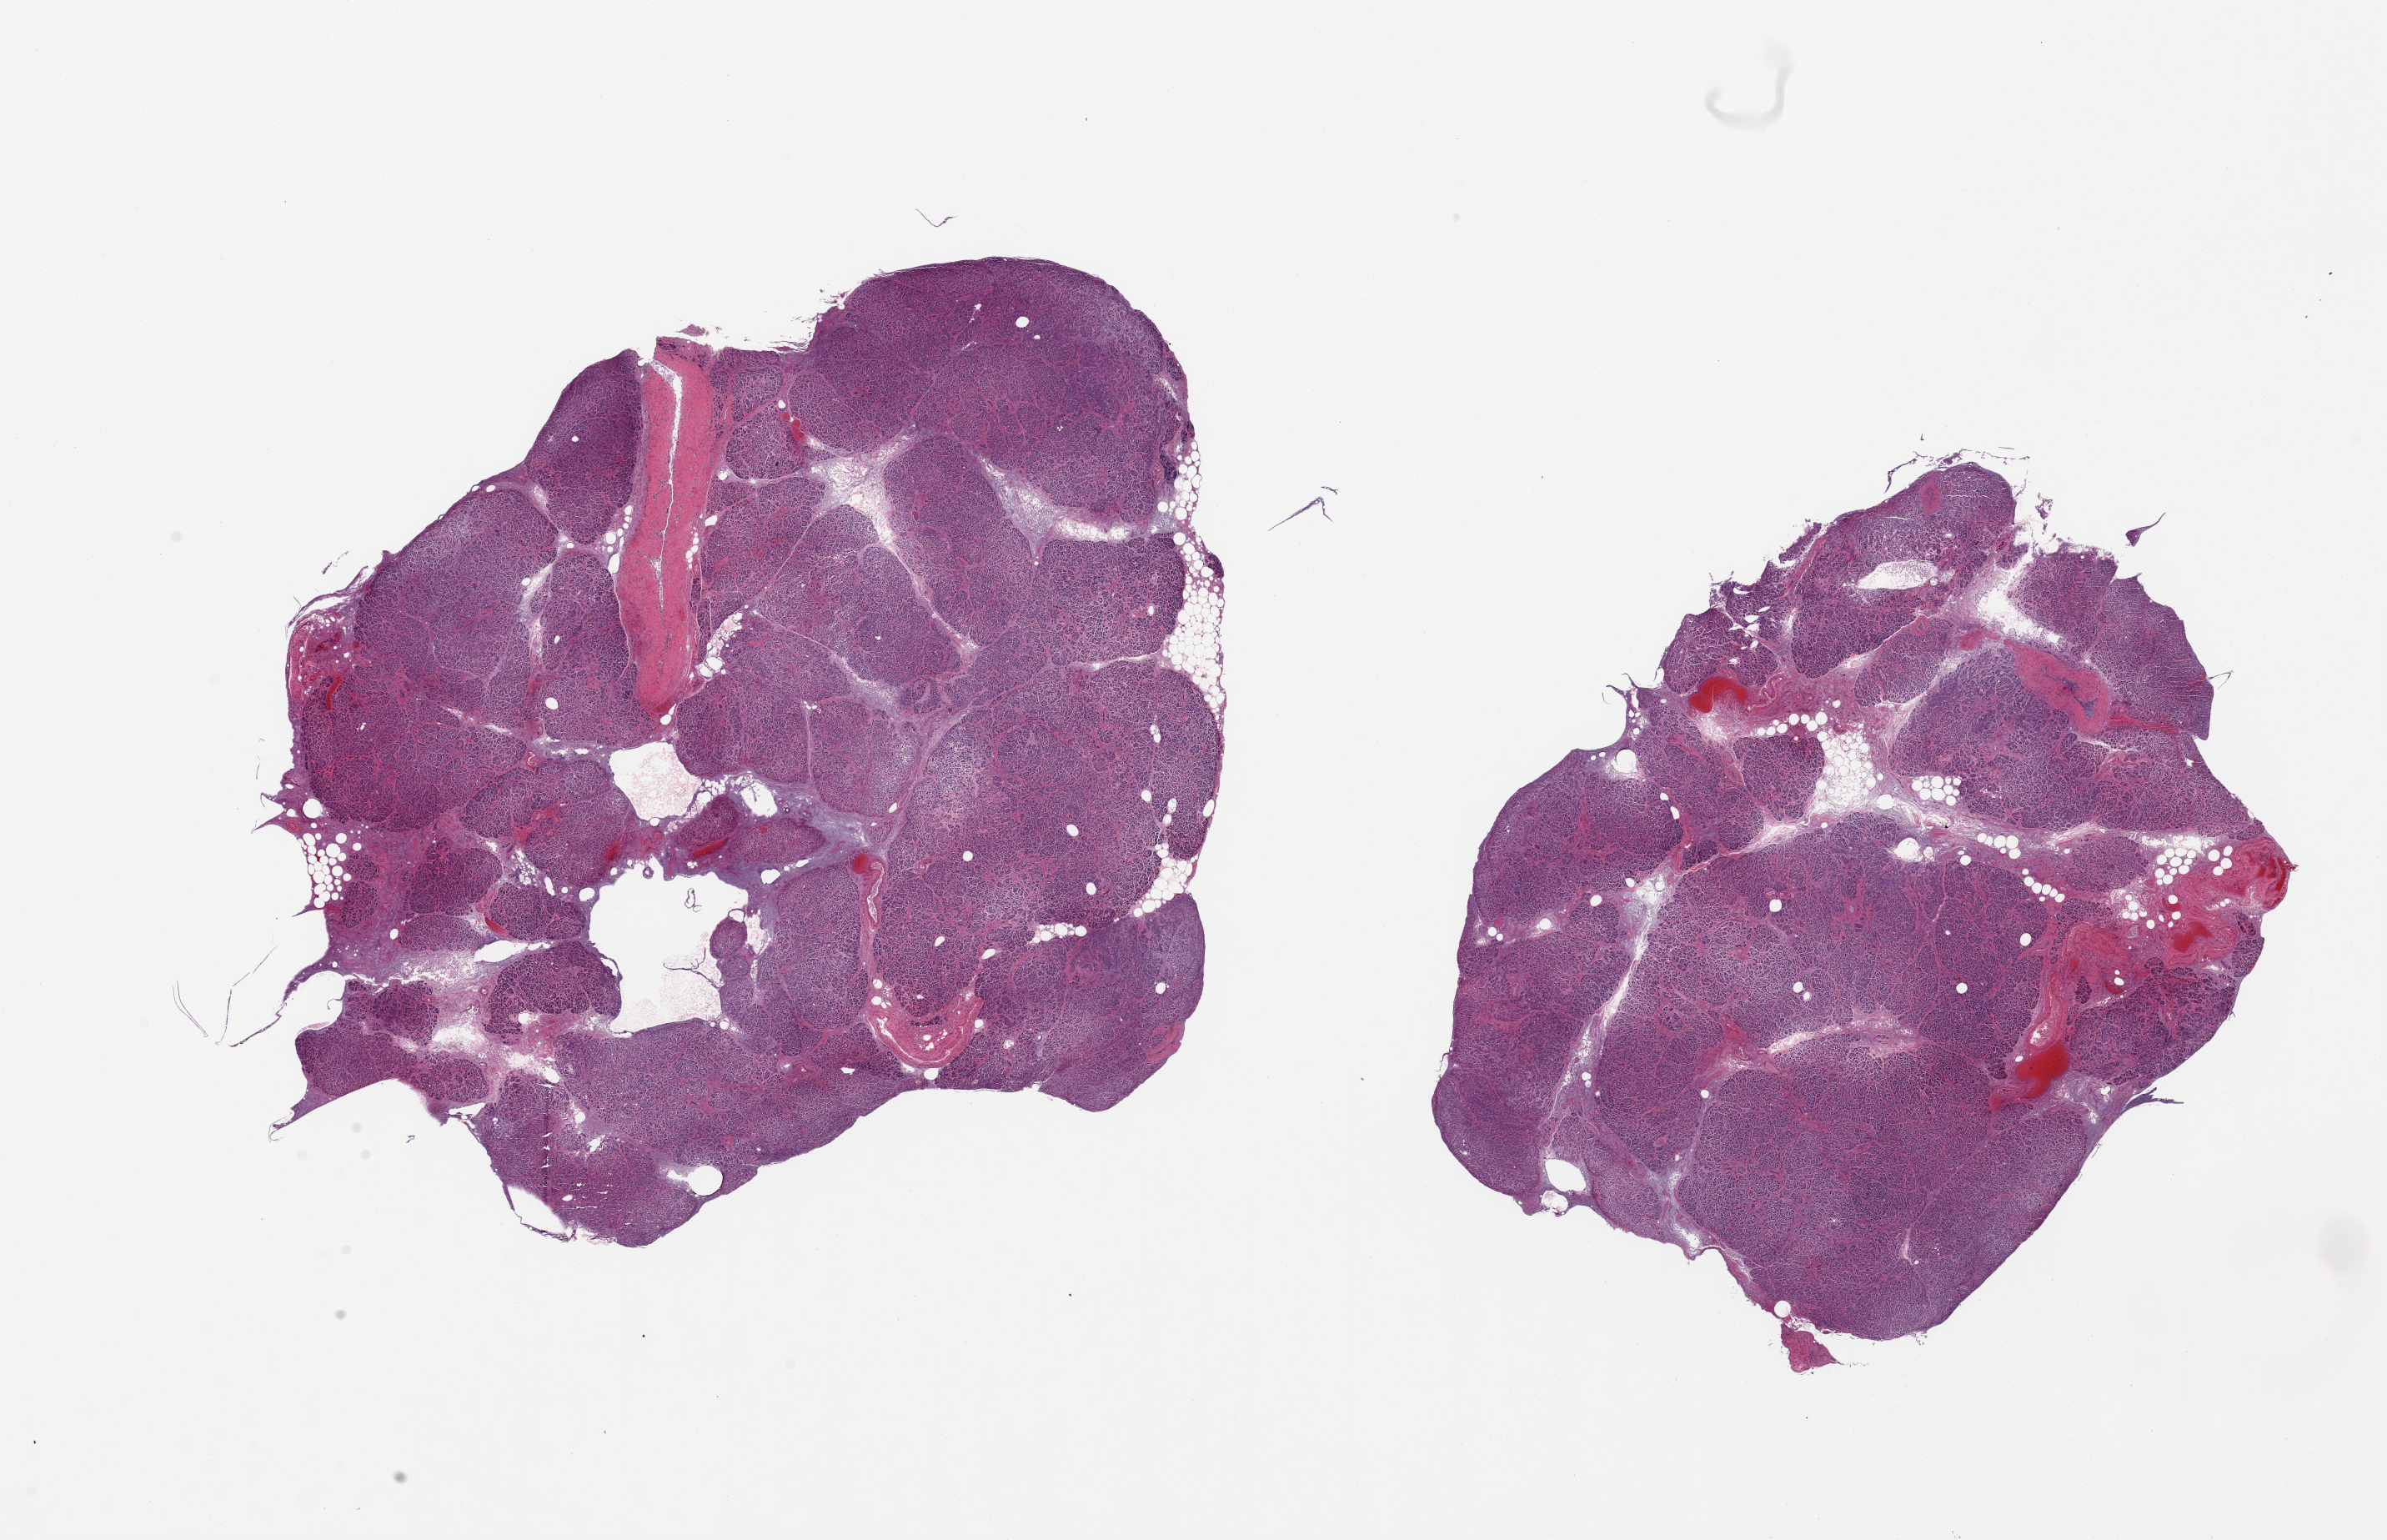
H&E whole-slide image, brightfield, whole scanned area (about 22.6 x 14.6 mm, slide scanned at 20x) shown as a low-resolution overview, PAXgene-fixed, paraffin-embedded tissue, sampled site (target tissue): pancreas, donor tissue sample. Donor sex: female.
Reviewer comment on this tissue sample: 2 pieces; severe autolysis.